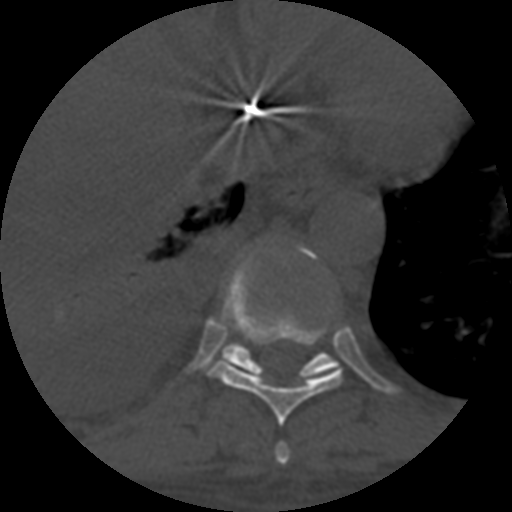
CT including the spine, one axial slice; position 371 of 708 along the scan axis; reconstruction kernel STANDARD; 120 kVp; one of 3 acquisitions stored at this slice position; bone window (W 1800 / L 400 HU); 1.25 mm slice thickness; 512 × 512 image matrix, field of view 160 × 160 mm. Patient age 55 years. Case-level facts recorded for this patient, not image findings: primary cancer: colon; vertebrae with lytic lesions (as recorded): T12, L1, L5.
Annotated regions visible in this slice (semi-automatically segmented with operator editing):
- T10 vertebra: box from (x=221, y=344) to (x=340, y=380) px
- T8 vertebra: (x=275, y=443)–(x=290, y=465)
- T9 vertebra: (x=209, y=248)–(x=343, y=426)